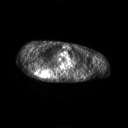
FDG PET of an extremity soft-tissue mass (from a PET/CT study), one axial slice. Slice 184 of 267 in the series (ordered by position). 3.27 mm slice thickness. 128 × 128 image matrix, field of view 700 × 700 mm. Patient: male, 61 years. Case-level facts recorded for this patient, not image findings: histological type: pleiomorphic spindle cell undifferentiated; grade: high; site of the primary tumour: right parascapusular.
Annotated regions visible in this slice (expert contour drawn on MRI and transferred to this co-registered scan by the dataset authors):
- gross tumour volume including surrounding oedema: bounding box <33,68,57,79> (left, top, right, bottom; pixels)
- gross tumour volume (mass): <34,68,51,78>